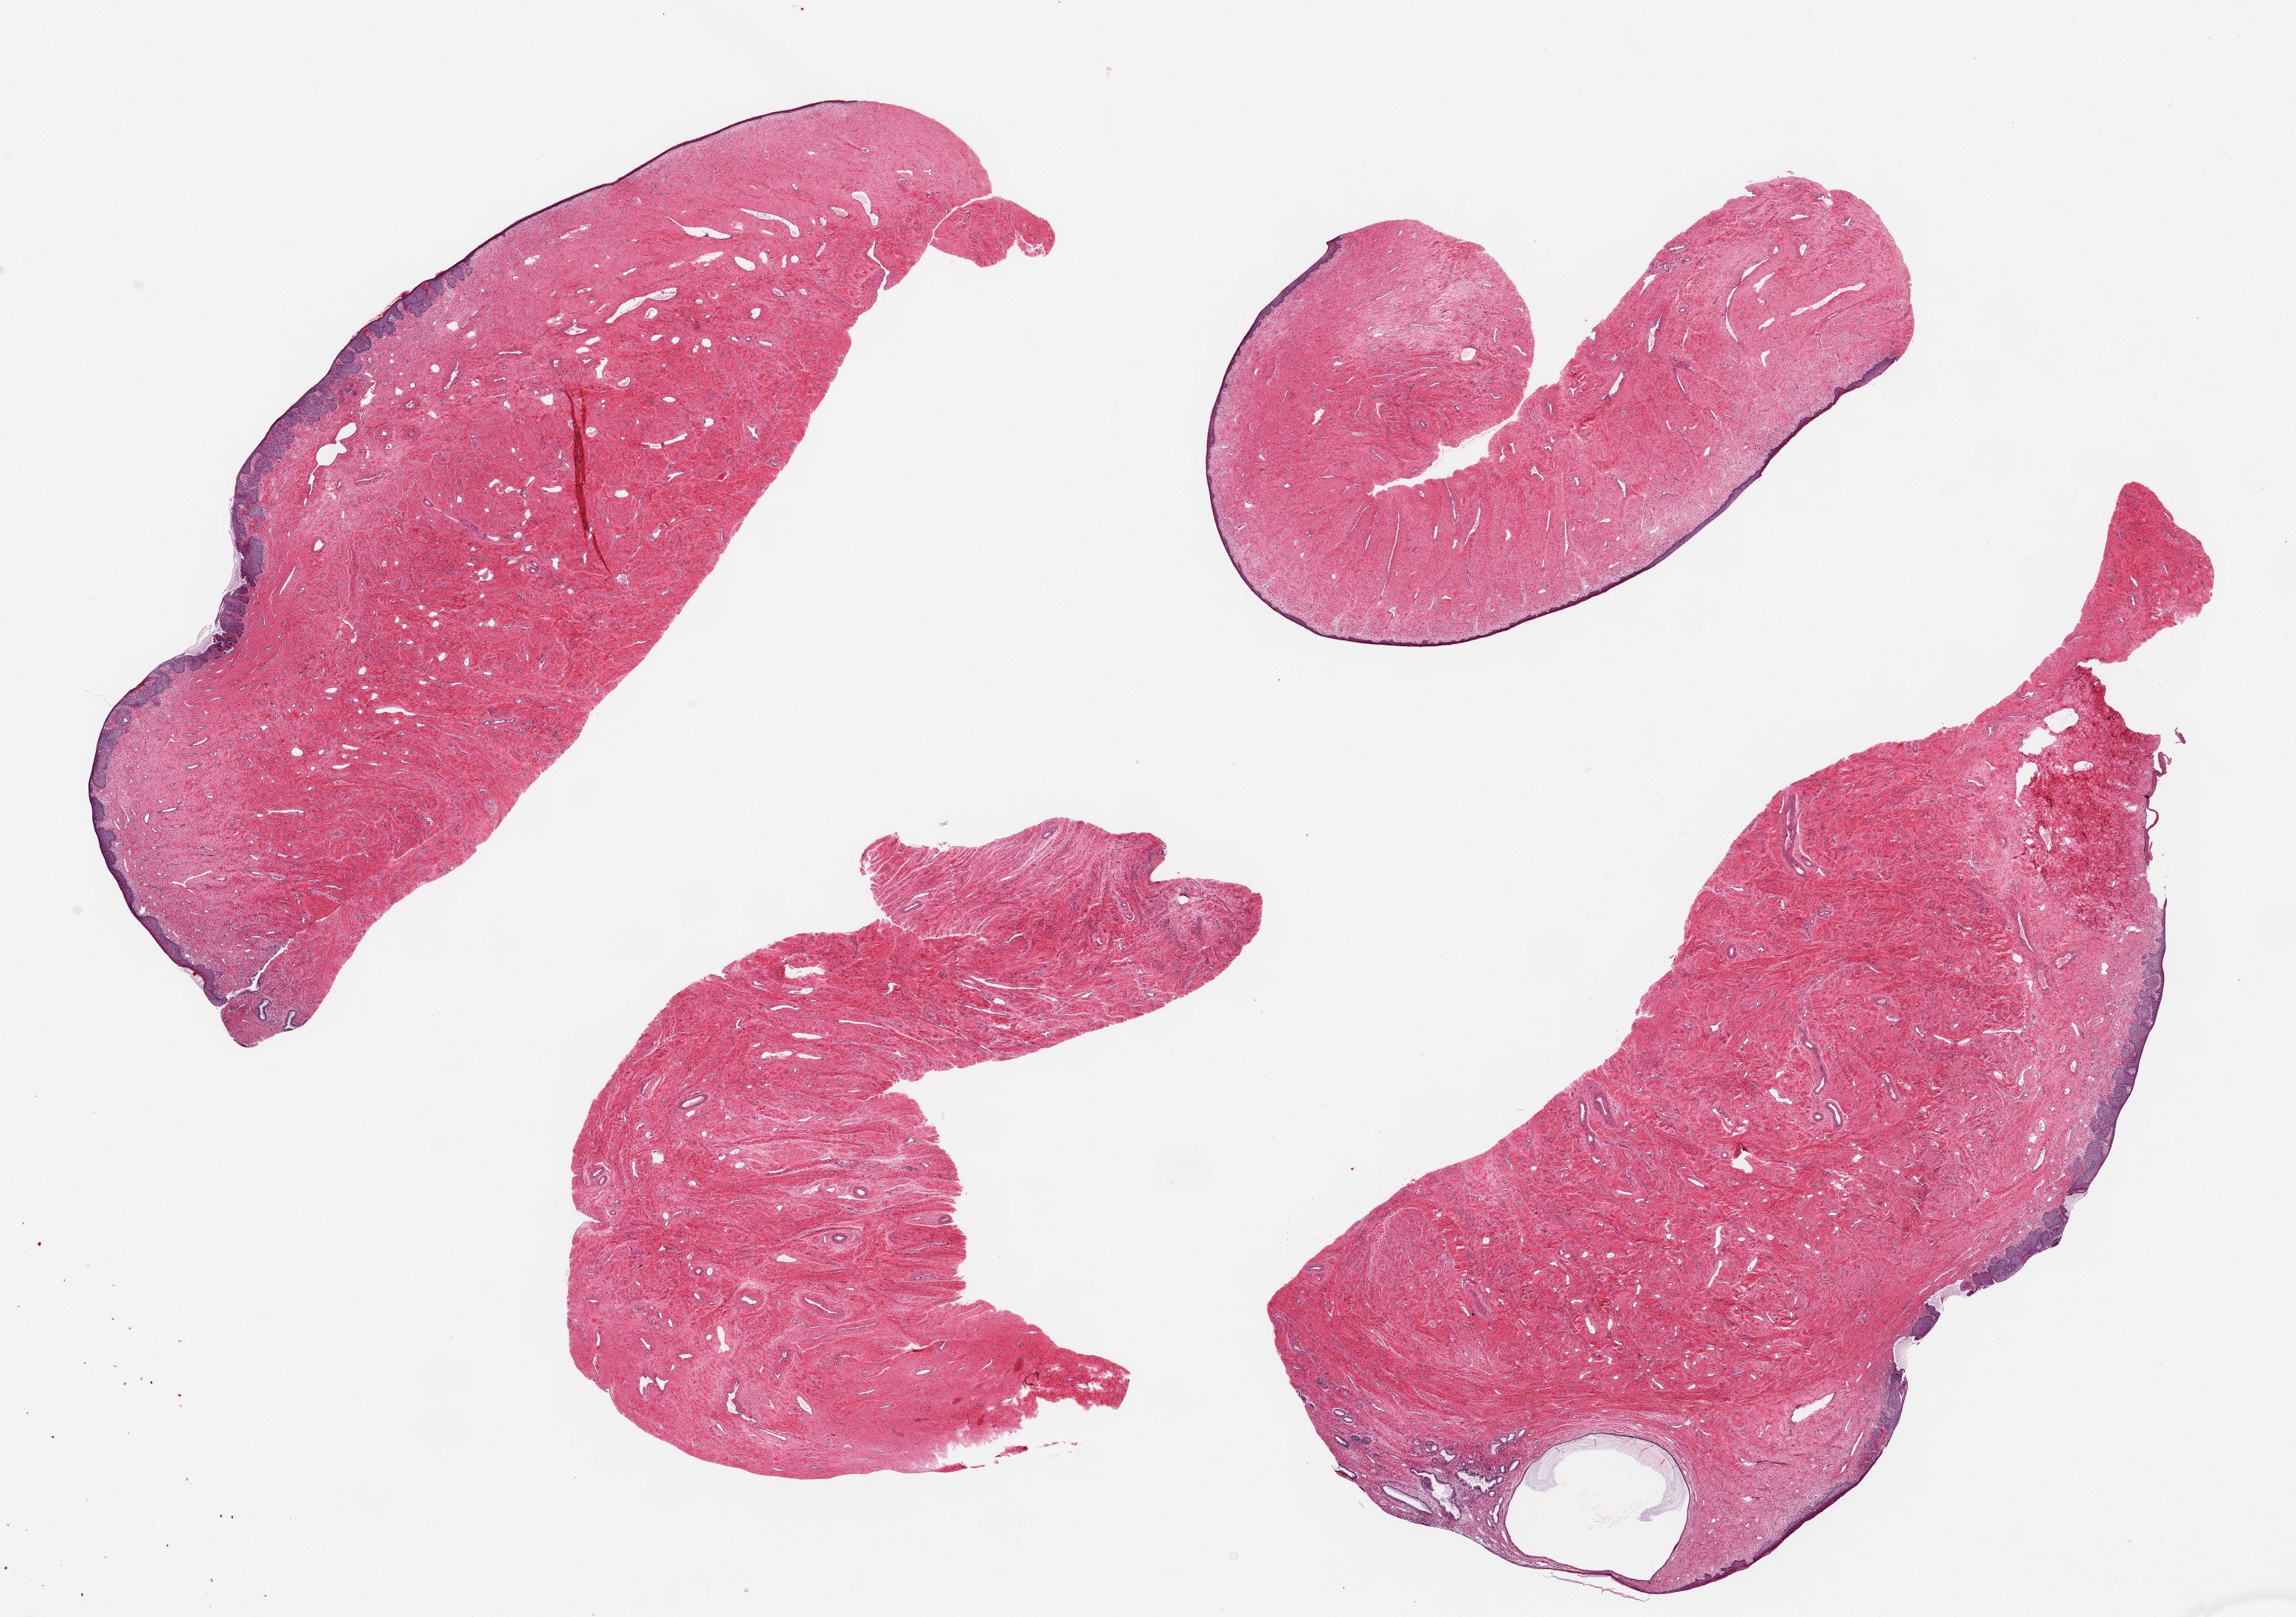
H&E whole-slide image, low-resolution overview of the scanned area, about 24.6 x 17.3 mm. PAXgene-fixed paraffin-embedded (PFPE) section. Section of exocervix (target tissue). Donor tissue sample. Female donor.
Pathologist's review note for this sample: 4 ~11x4.5mm aliquots. Mainly squamous, focal glandular mucosa (transition zone), ~5-8% of thickness.